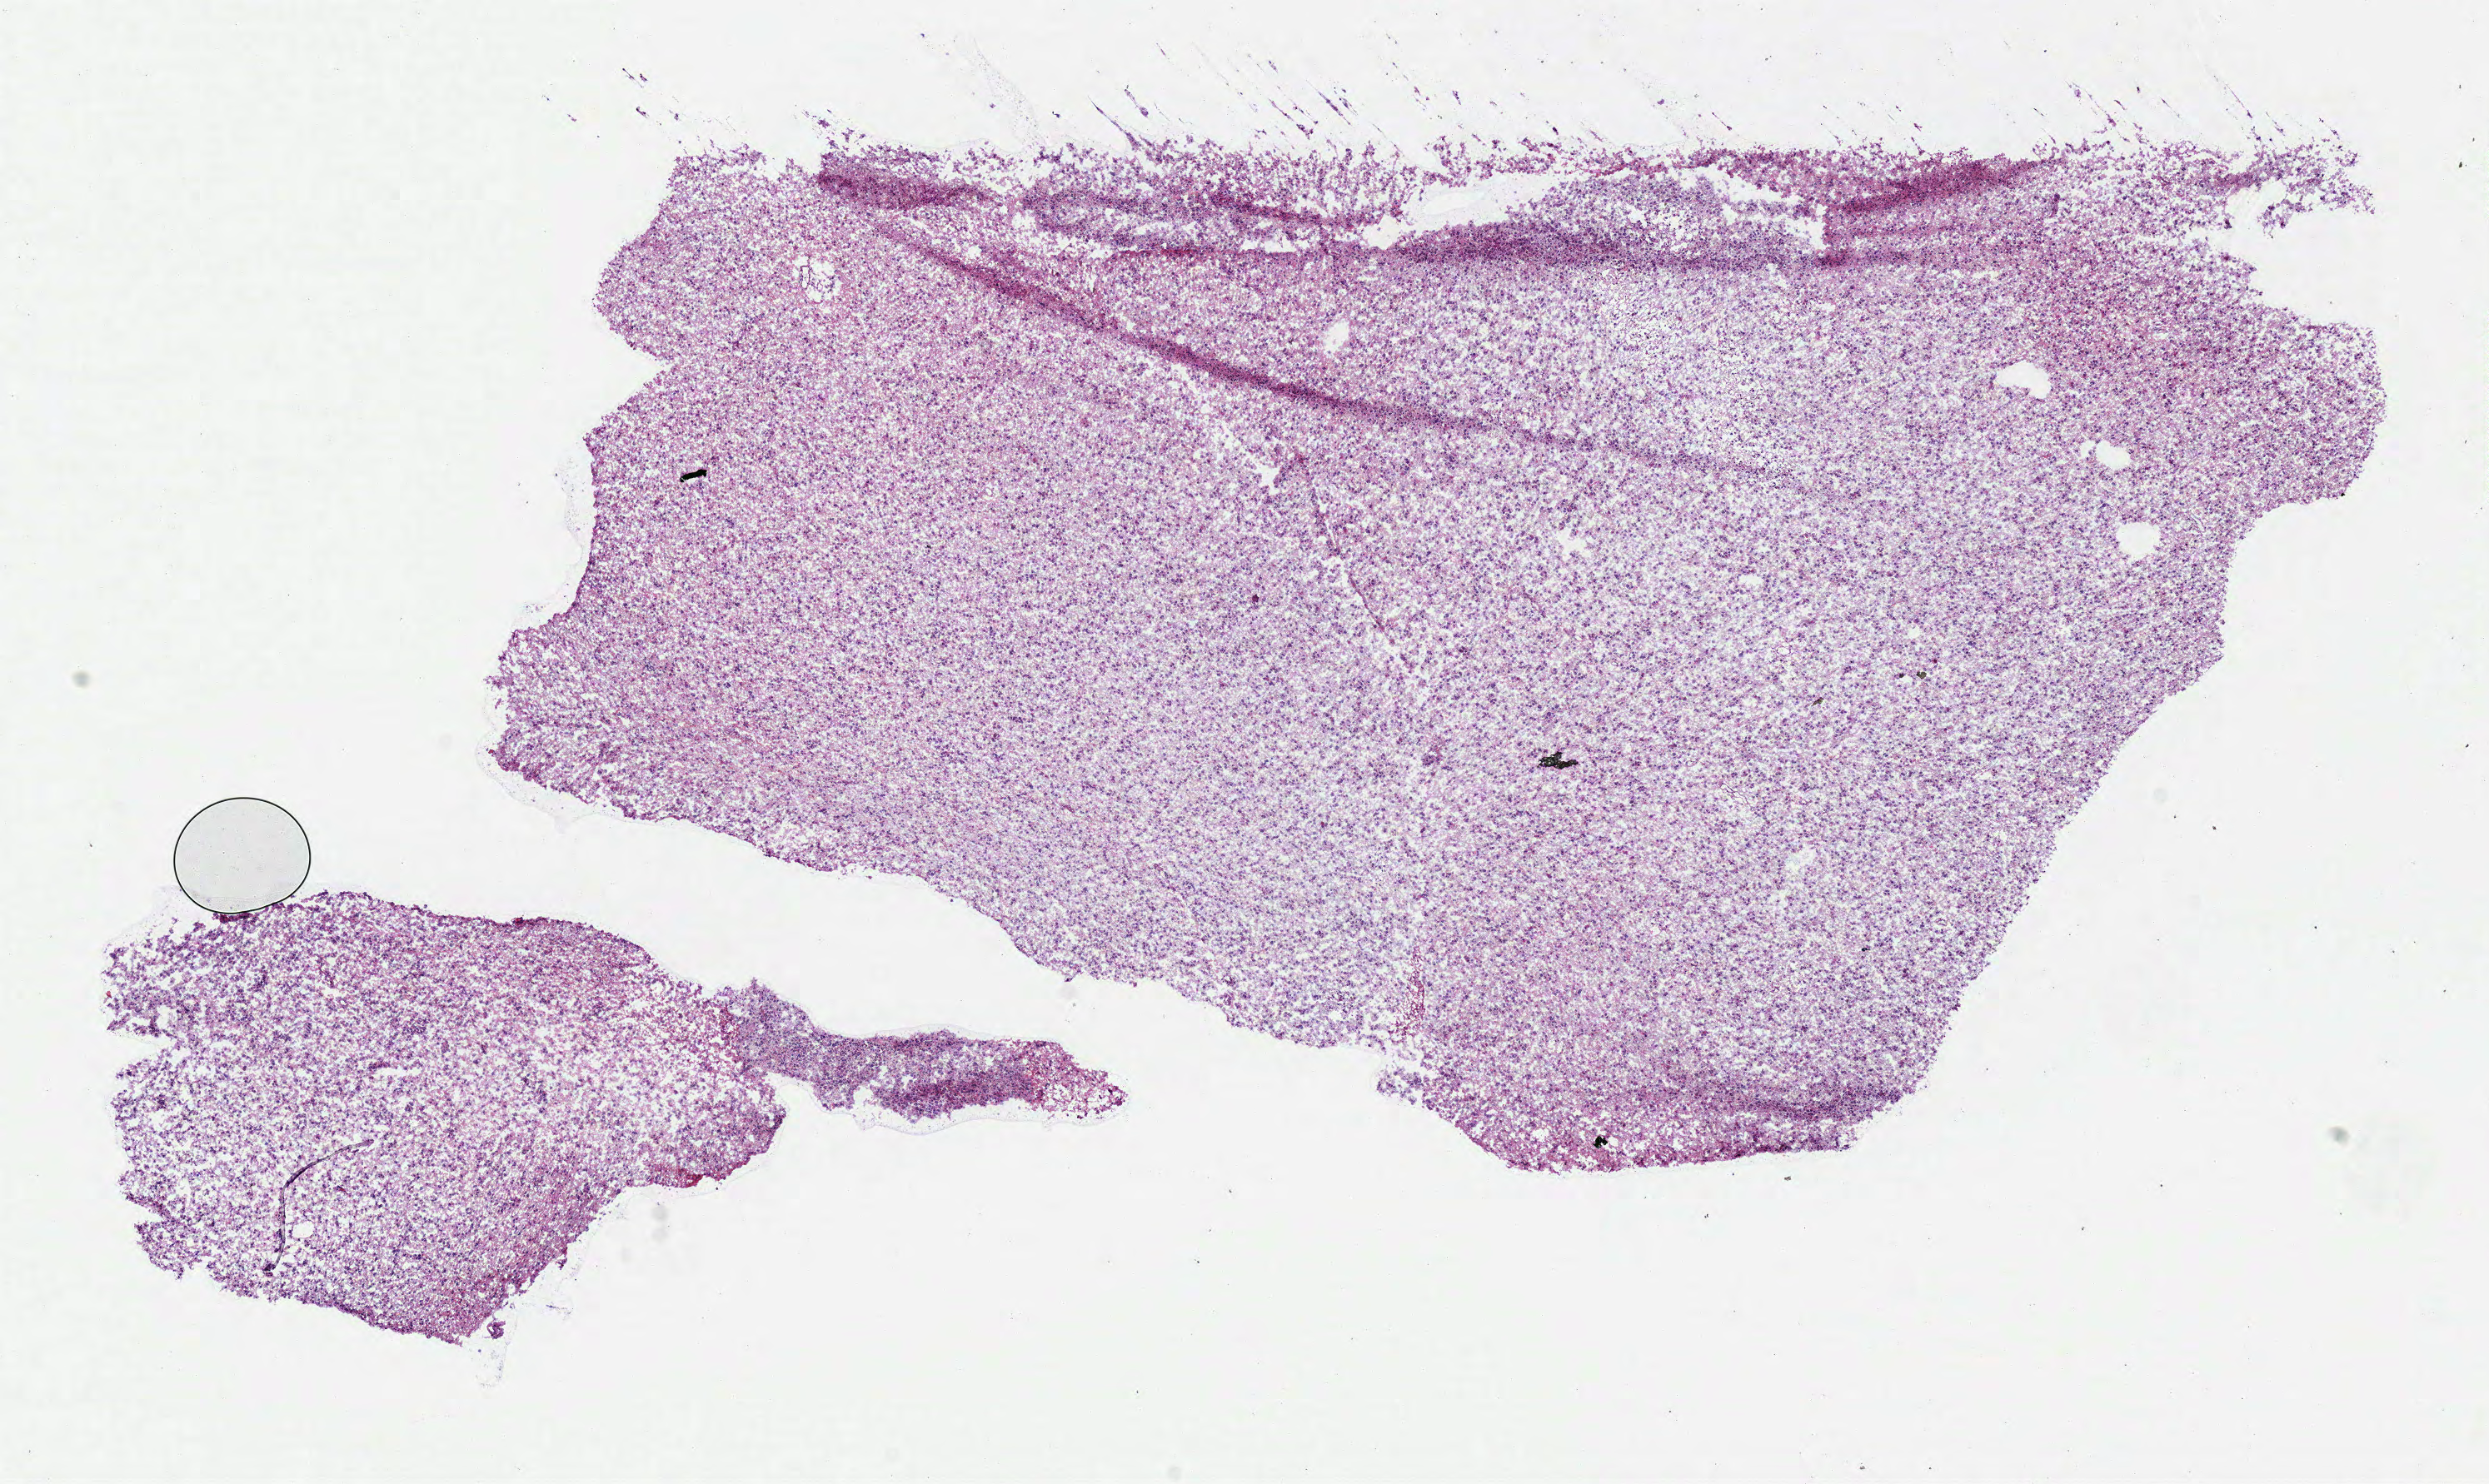
Digitized H&E tissue section (whole slide) — low-resolution overview of the scanned area, about 11.7 x 7.0 mm (slide scanned at 40x), frozen section from the bottom of the tissue portion, brain, primary tumour sample. Male, age 54 years at initial diagnosis. Histologic grade: G2 (moderately differentiated). Pathologist review of this section (percent, as recorded): tumour cells 100%, tumour nuclei 80%, normal cells 0%, stromal cells 0%, necrosis 0%.
Histologic diagnosis: Oligodendroglioma, NOS (cerebrum).